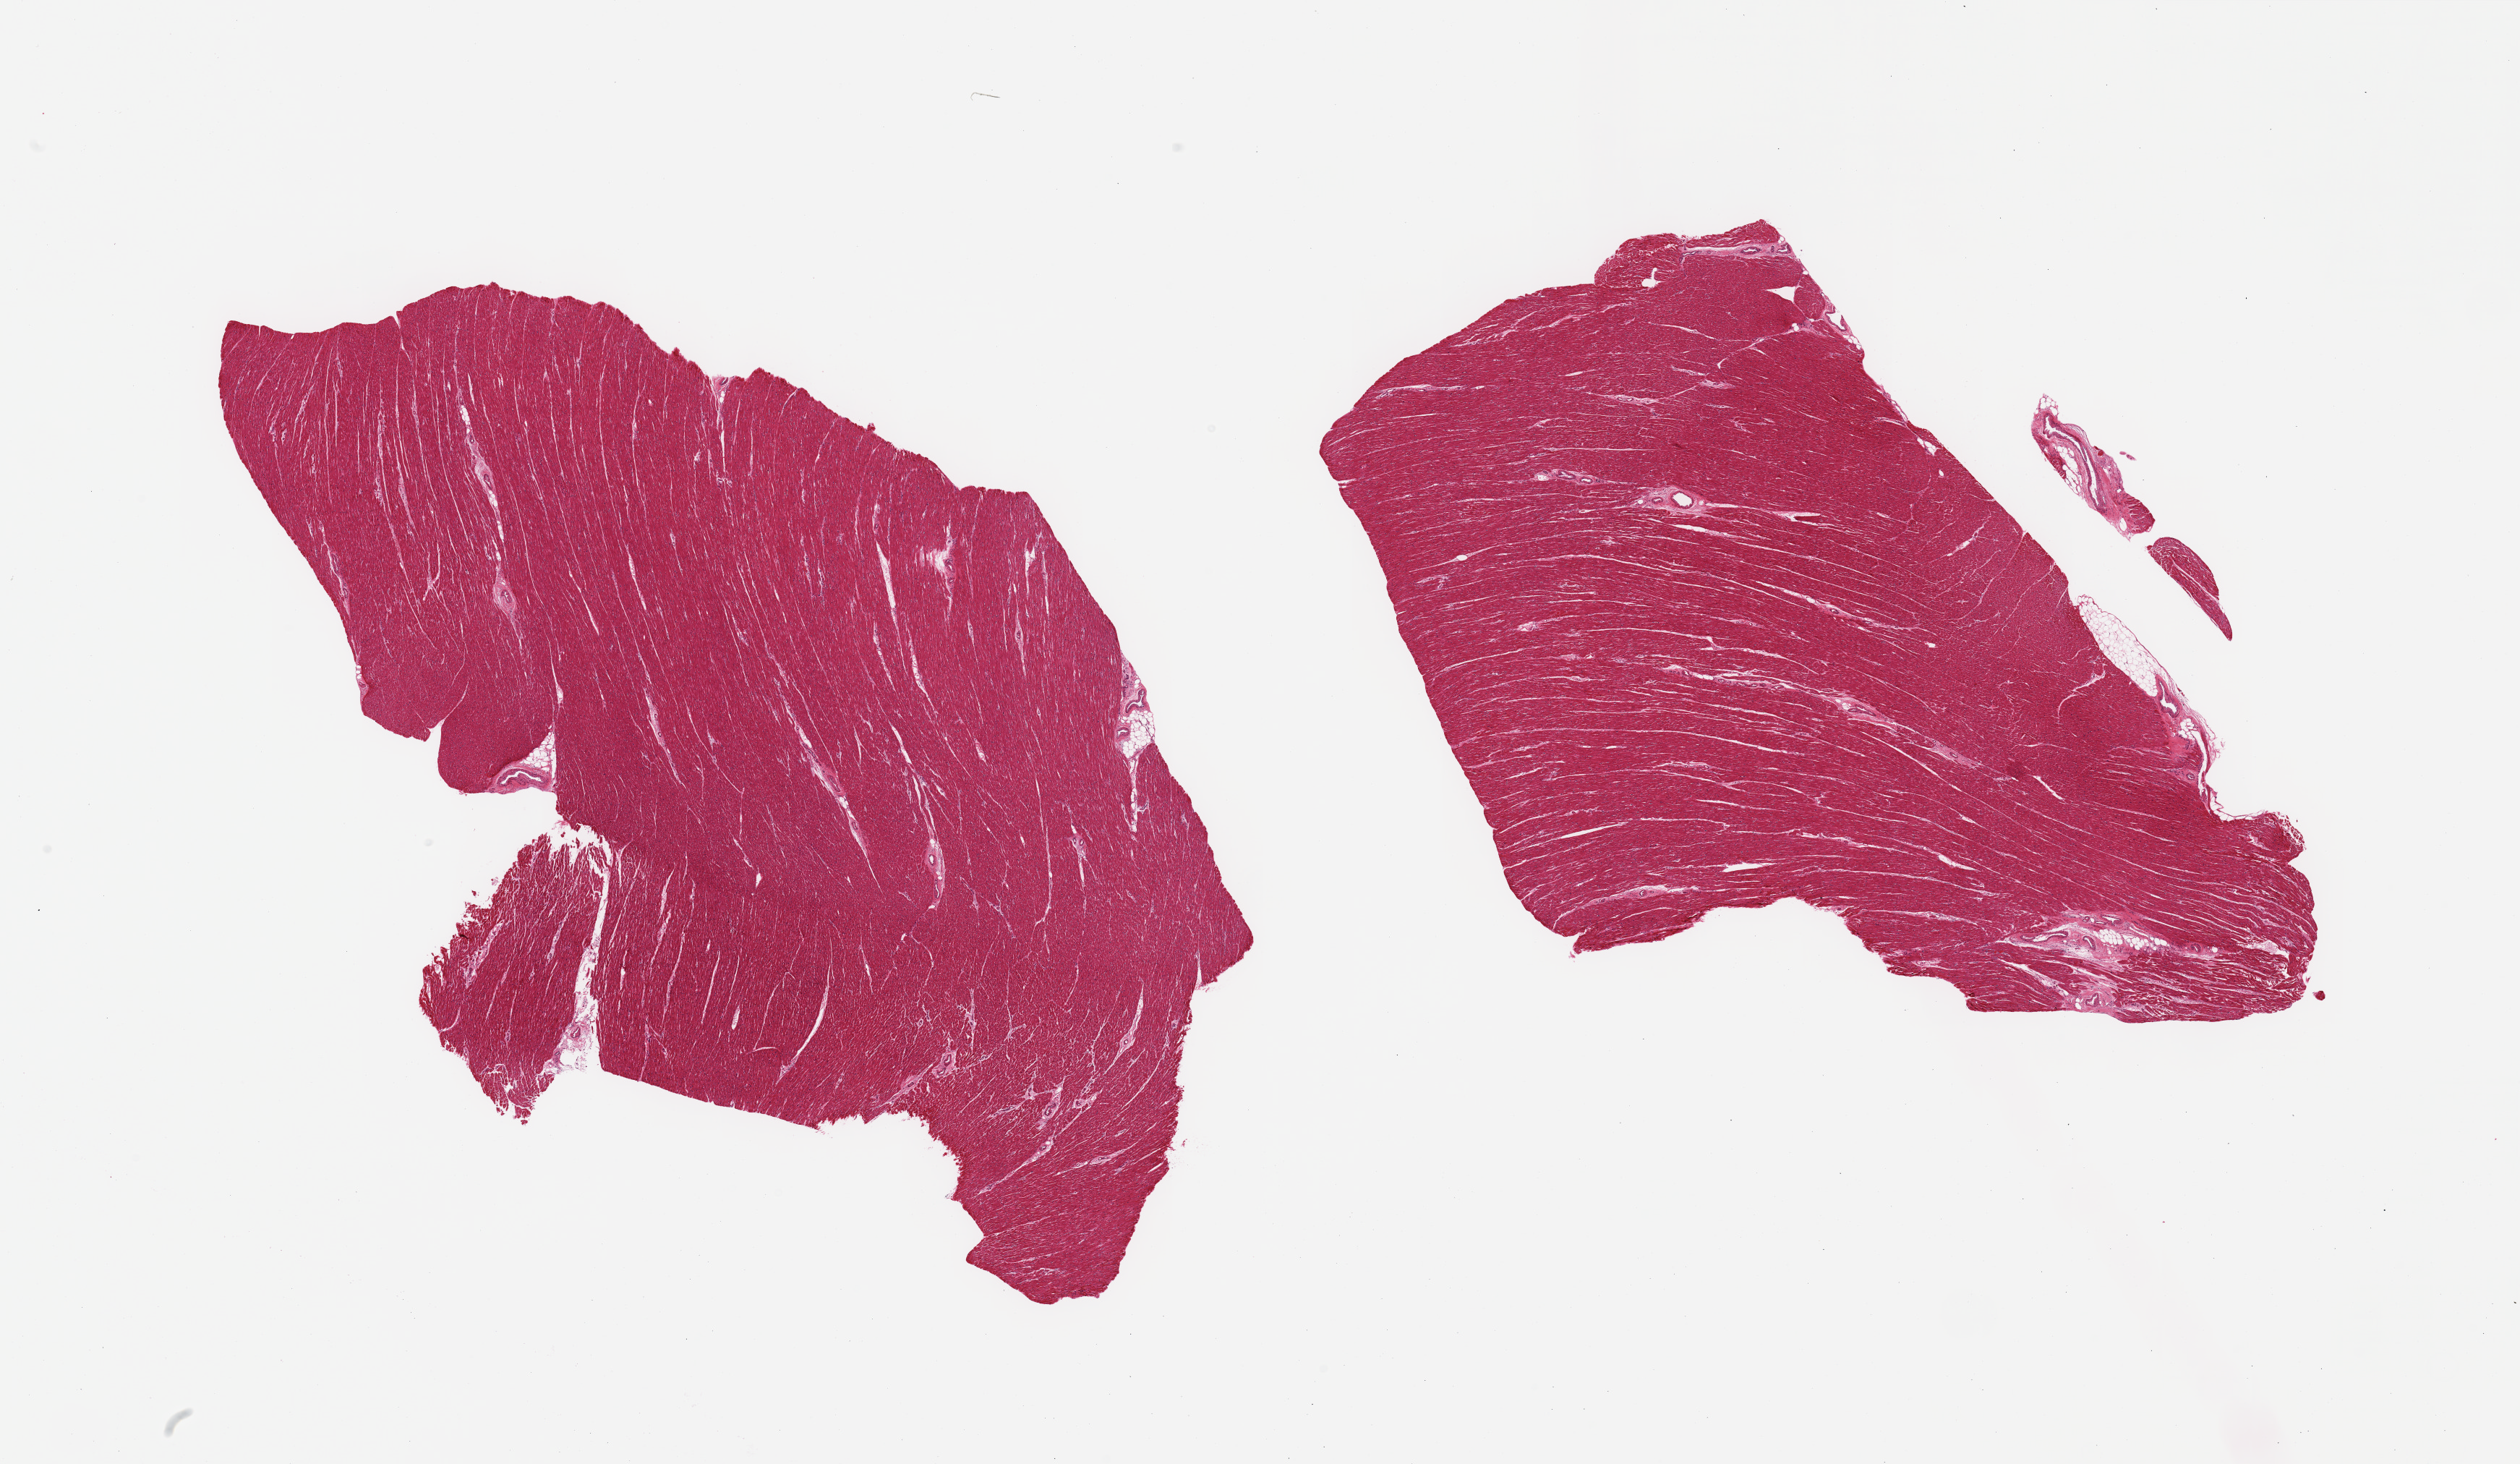
Whole-slide image, haematoxylin and eosin stain, a low-resolution overview of the entire scanned area, about 27.6 x 16.0 mm. PAXgene-fixed, paraffin-embedded tissue. Target tissue: heart. Donor tissue sample. Donor: female.
Review note (as recorded): 2 pieces; subtle interstitial/perivascular connective tissue accentuation; well trimmed.